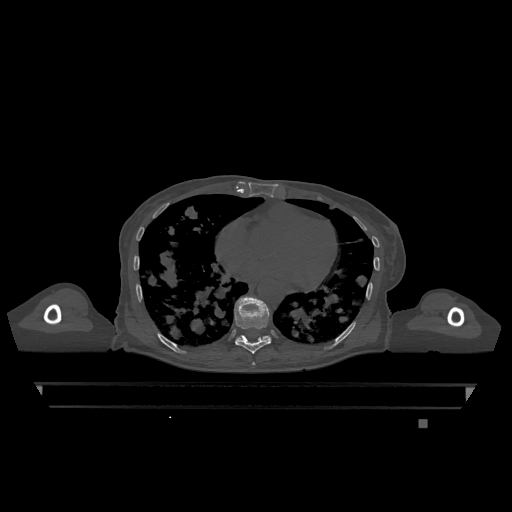
CT including the spine, one axial slice; position 682 of 1317 along the scan axis; bone window (W 1800 / L 400 HU); 0.5 mm slice thickness; 512 × 512 image matrix. Patient: female, 74 years. From the clinical record (not read from this slice): primary cancer: lung; vertebrae with lytic lesions (as recorded): T1, T4, T5, T6, L4, L5.
Outlined on this slice (semi-automatically segmented with operator editing):
- T10 vertebra: bounding box (x1, y1, x2, y2) in pixels: (237, 335, 270, 340)
- T7 vertebra: (252, 362, 255, 366)
- T9 vertebra: (234, 296, 271, 354)